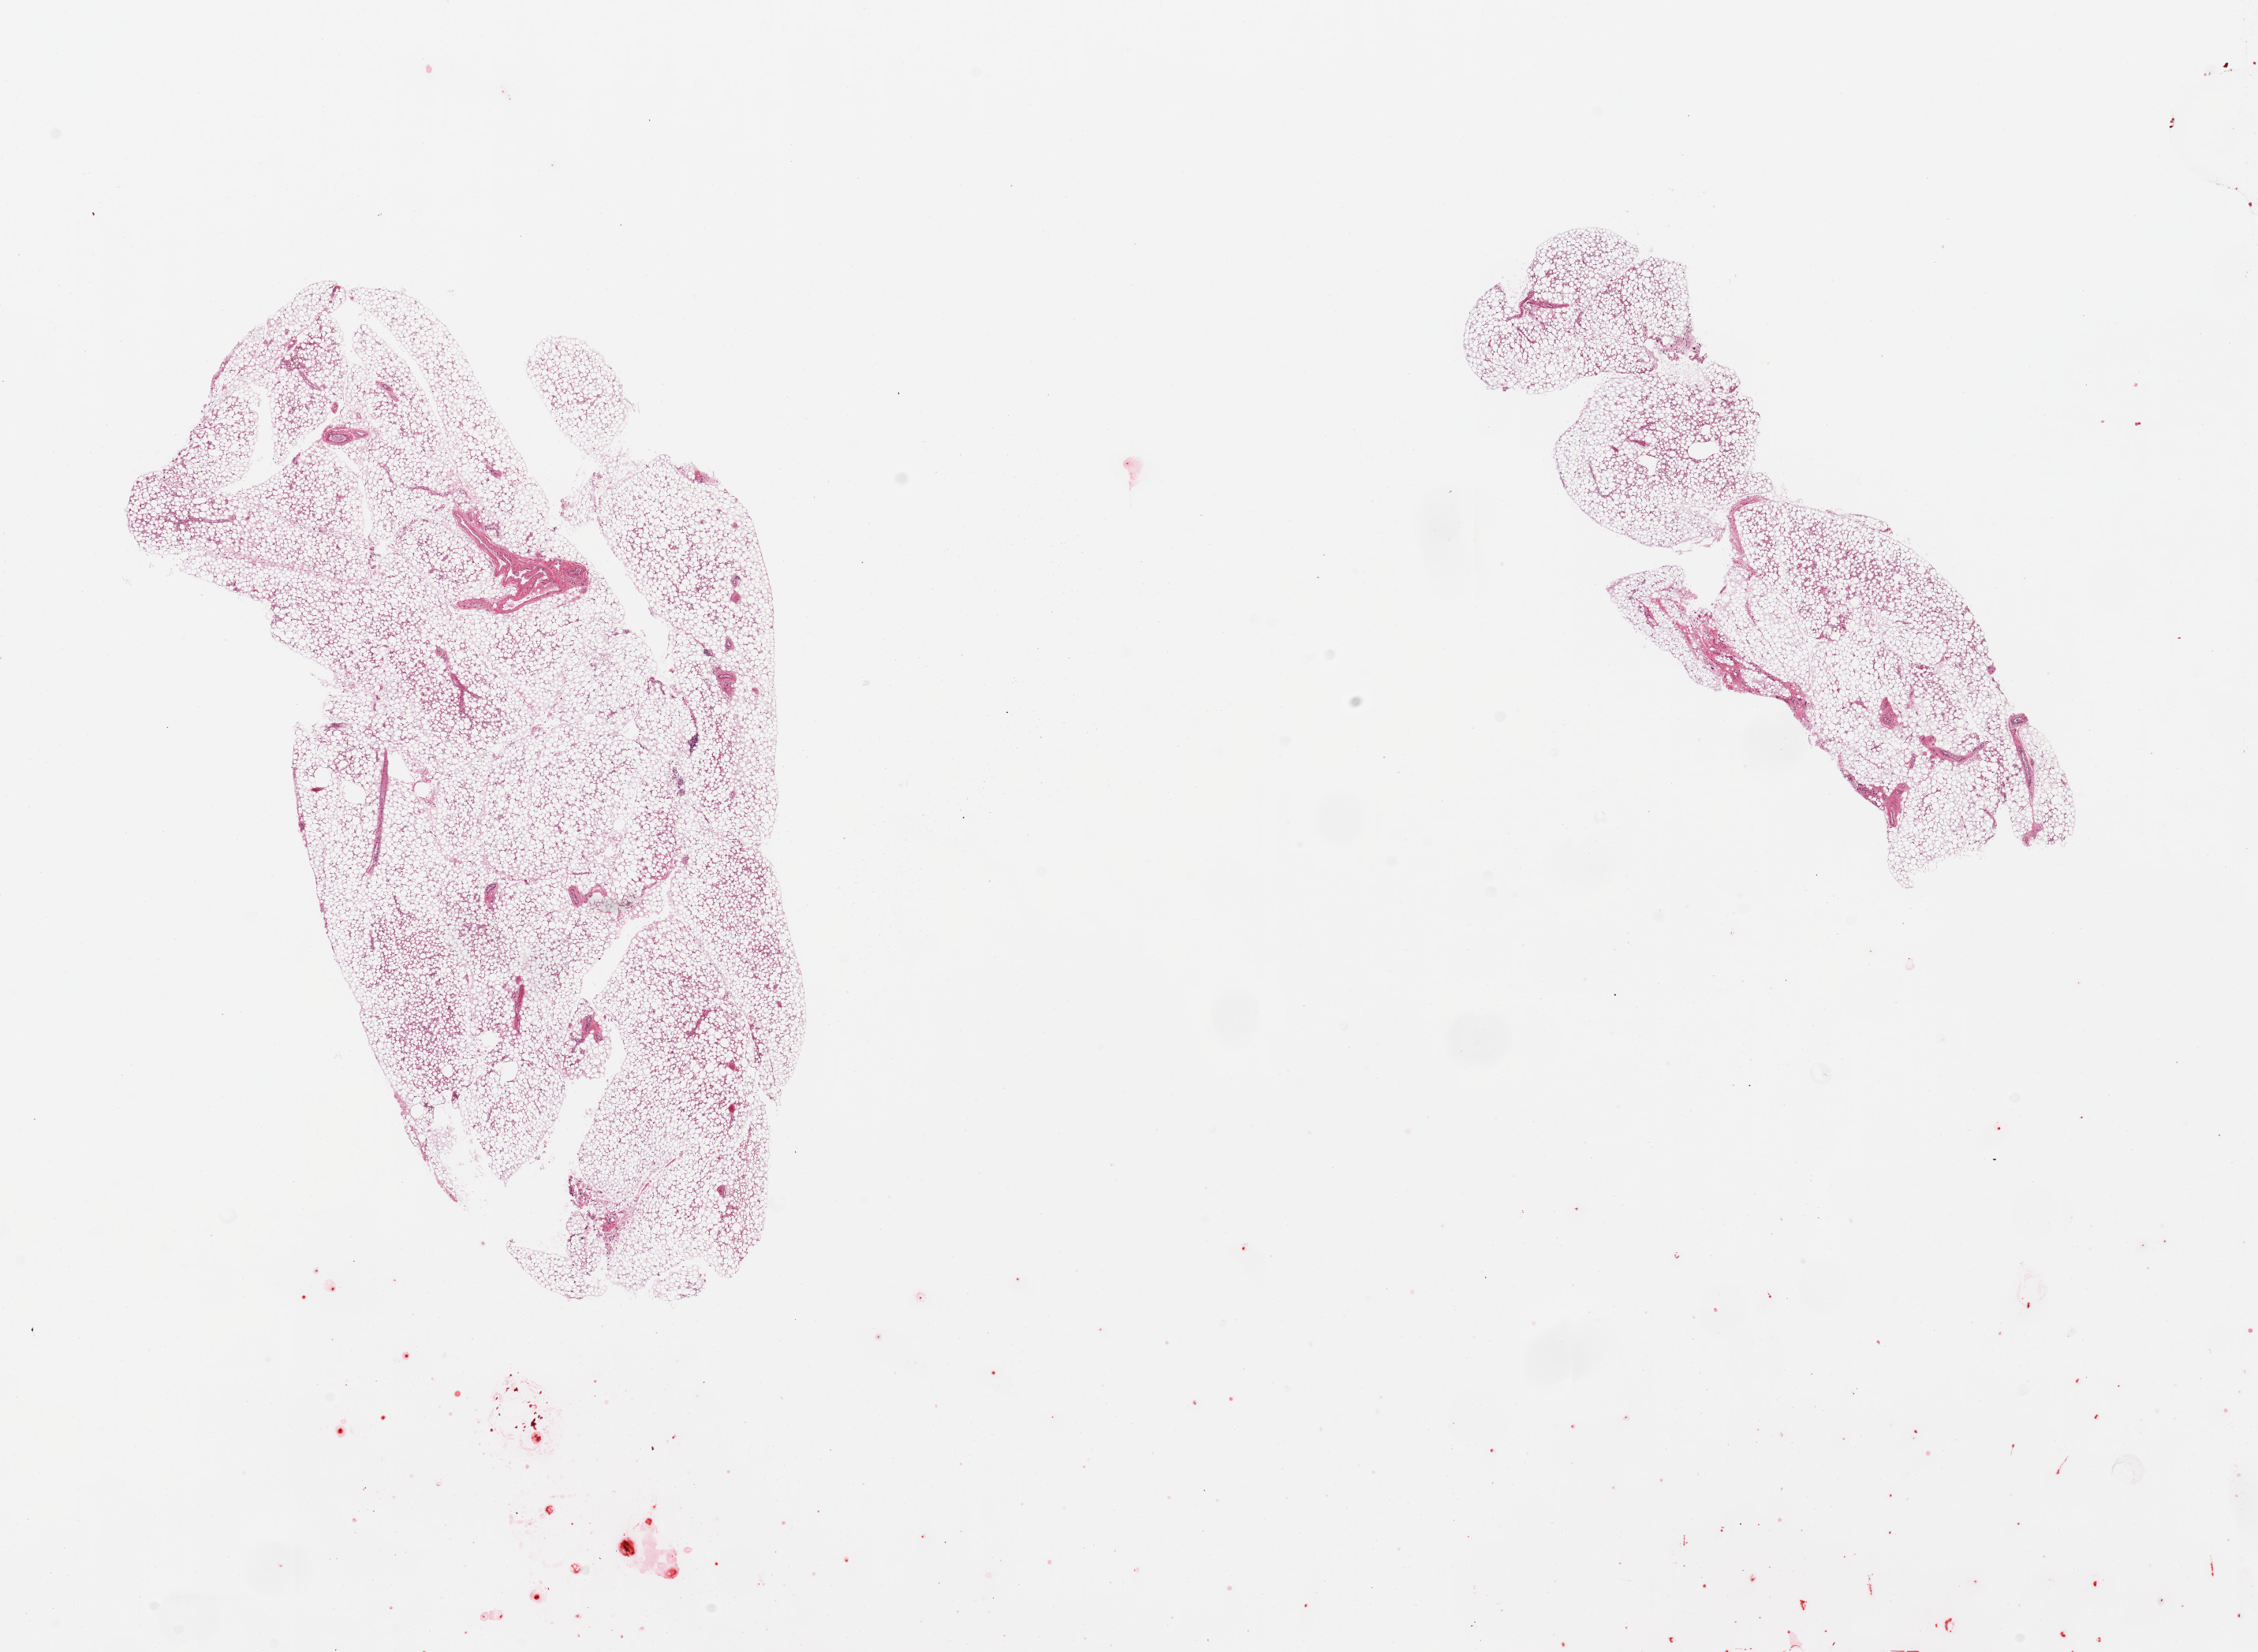
Digitized haematoxylin and eosin-stained section, shown as a low-resolution overview of the whole scanned area (about 22.6 x 16.6 mm, slide scanned at 20x); PAXgene-fixed, paraffin-embedded tissue; section of adrenal gland (target tissue); donor tissue sample. Donor sex: female.
Review note (as recorded): 2 pieces; no adrenal; only fat.